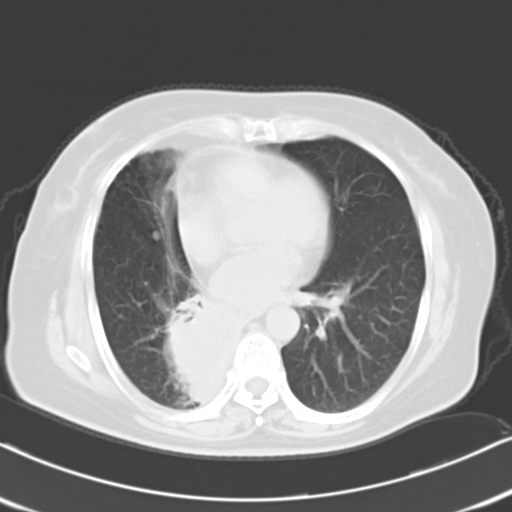
Chest CT, one axial slice; slice 9 of 21 in the series (ordered by position); lung window (W 1500 / L -600 HU); 10 mm slice thickness; 512 × 512 image matrix. Patient: female, 61 years. From the clinical record (not read from this slice): clinical TNM (as recorded): T1b N0 M1b.
Outlined on this slice (bounding box drawn by a radiologist):
- lung tumour (recorded histology: squamous cell carcinoma): bounding box <160,285,259,423> (left, top, right, bottom; pixels)